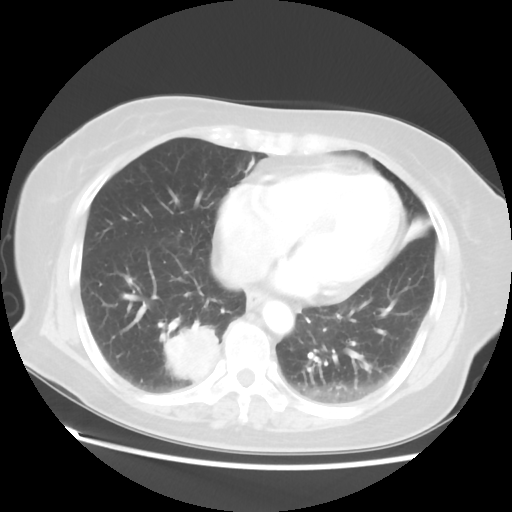
Chest CT, one axial slice. Position 19 of 52 along the scan axis. Reconstruction kernel STANDARD. 120 kVp. Lung window (W 1500 / L -600 HU). 5 mm slice thickness. 512 × 512 image matrix, field of view 356 × 356 mm. Patient: female, 69 years. Case-level facts recorded for this patient, not image findings: clinical TNM (as recorded): T2 N1 M1a.
Structures marked on this image (rectangle marked by the reading radiologist):
- lung tumour (recorded histology: adenocarcinoma): box from (x=158, y=322) to (x=221, y=388) px